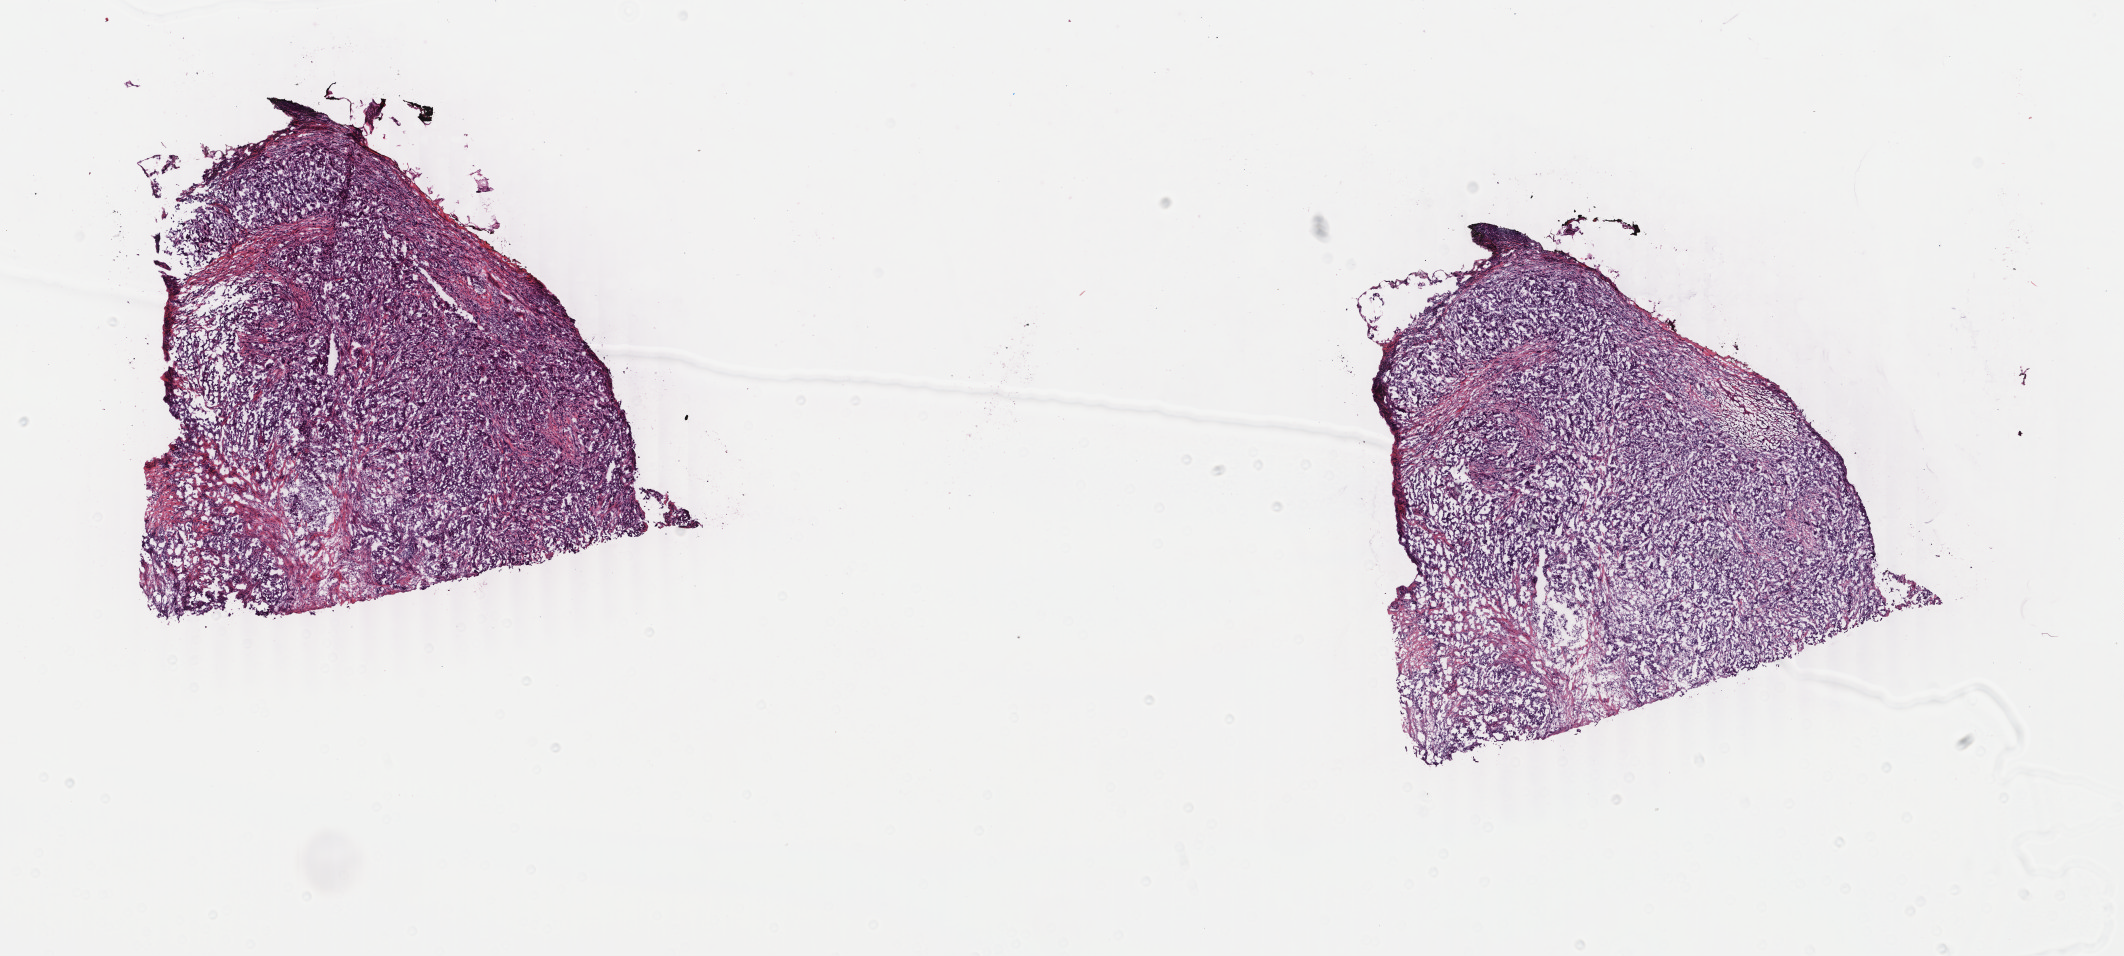
Whole-slide histology image, H&E-stained — a low-resolution overview of the entire scanned area, about 16.9 x 7.6 mm, frozen section from the top of the tissue portion, breast, primary tumour sample. Female, age 55 years at initial diagnosis. Composition of this section per pathologist review: tumour cells 80%, tumour nuclei 80%, normal cells 0%, stromal cells 15%, necrosis 5%. Infiltration values recorded for this section: lymphocyte infiltration 30%, monocyte infiltration 10%, neutrophil infiltration 20%.
AJCC pathologic stage: IIIC. Diagnosis: Infiltrating duct carcinoma, NOS.